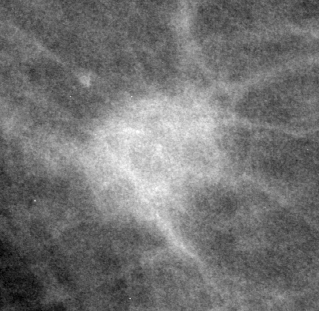
Cropped region of a digitized screen-film mammogram centred on a radiologist-marked abnormality; right breast; CC view.
Marked abnormality: mass, shape oval, margins spiculated; BI-RADS assessment category 5; subtlety rating 5 on a 1 (subtle) to 5 (obvious) scale; pathology result (as recorded, not read from the image): malignant.